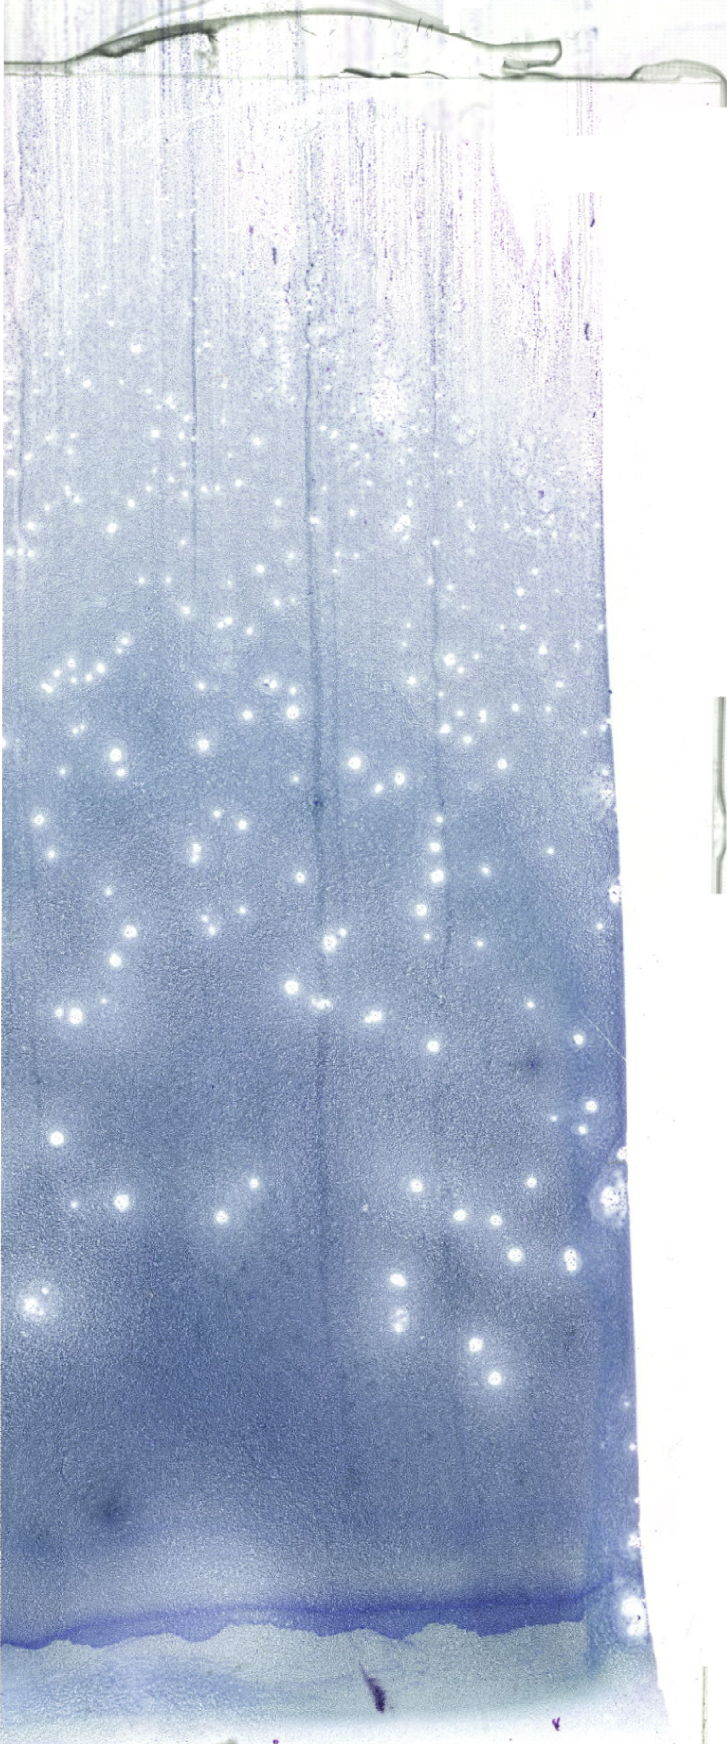
May-Grünwald–Giemsa-stained marrow aspirate smear (whole slide), whole scanned area (about 20.6 x 49.4 mm) shown as a low-resolution overview. Male patient.
Diagnosis: B Acute Lymphoblastic Leukemia.